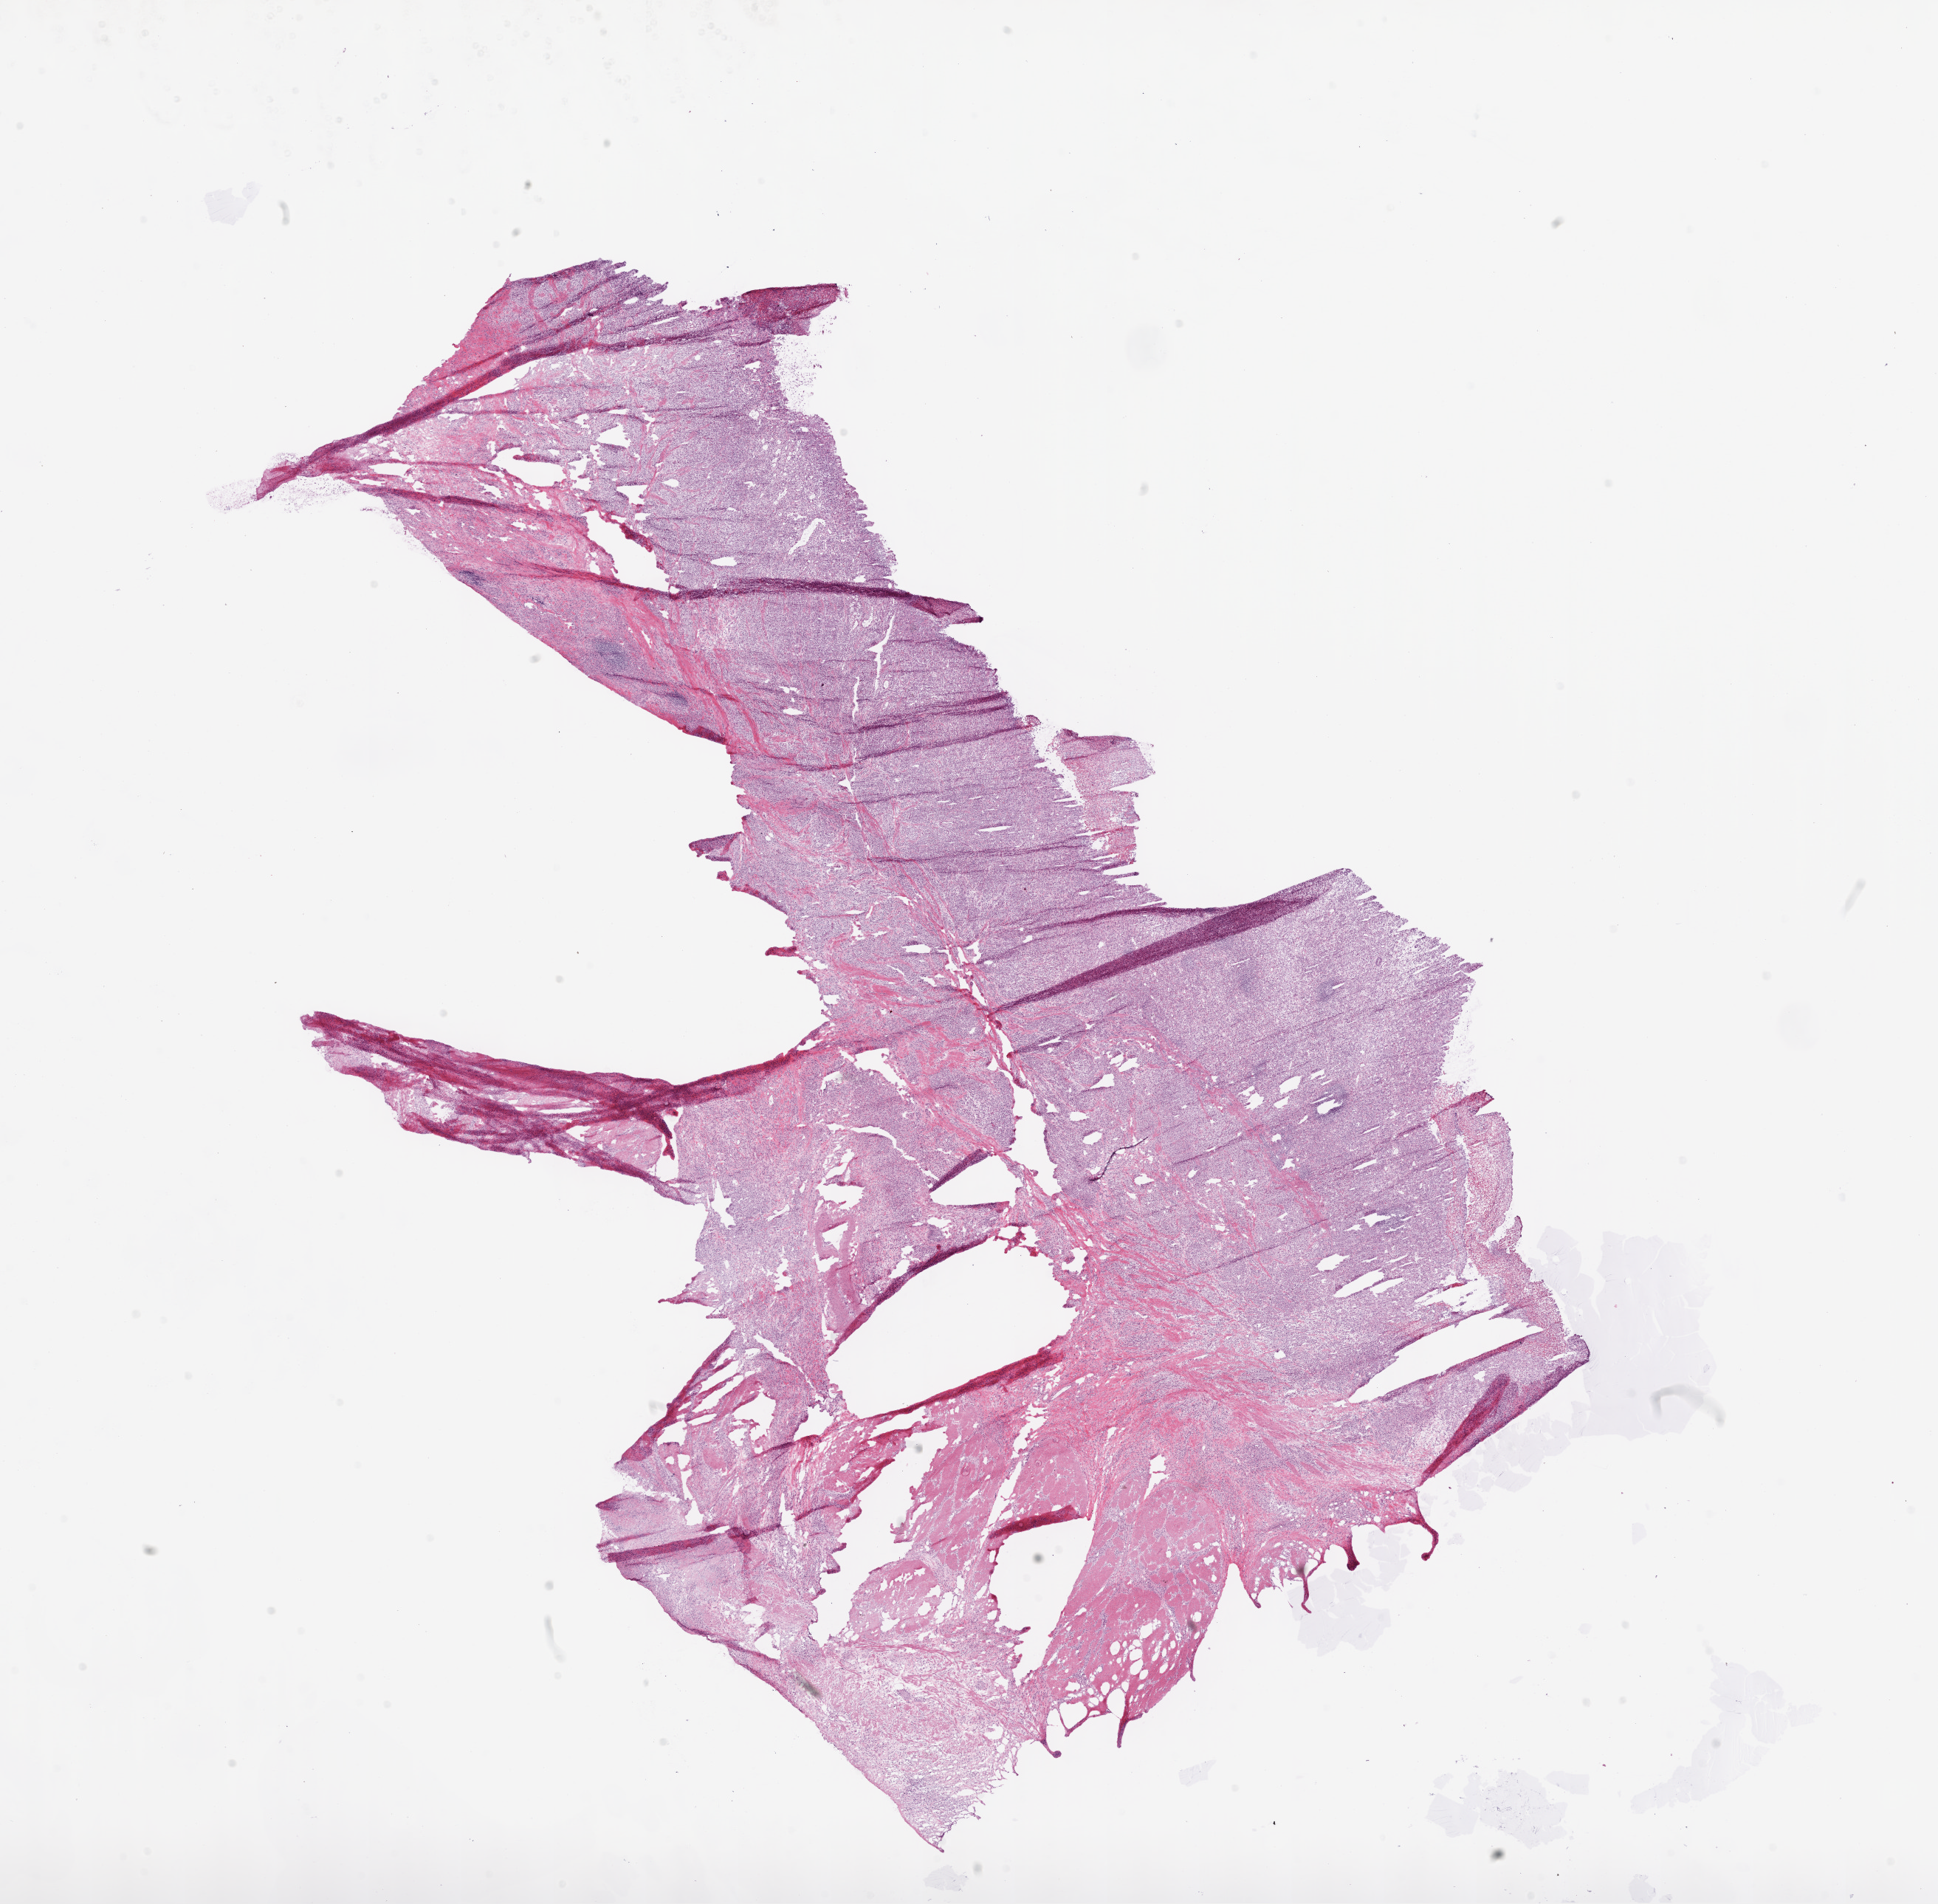
Digitized H&E-stained tissue section (whole slide) — shown as a low-resolution overview of the whole scanned area (about 21.1 x 20.7 mm, from a 20x scan), frozen section from the top of the tissue portion, stomach, primary tumour sample. Female, age 53 years at initial diagnosis. Histologic grade: G3 (poorly differentiated). Slide review estimates, as recorded: tumour cells 80%, tumour nuclei 85%, normal cells 10%, stromal cells 10%, necrosis 0%.
Histologic diagnosis: Adenocarcinoma, NOS (cardia, NOS).